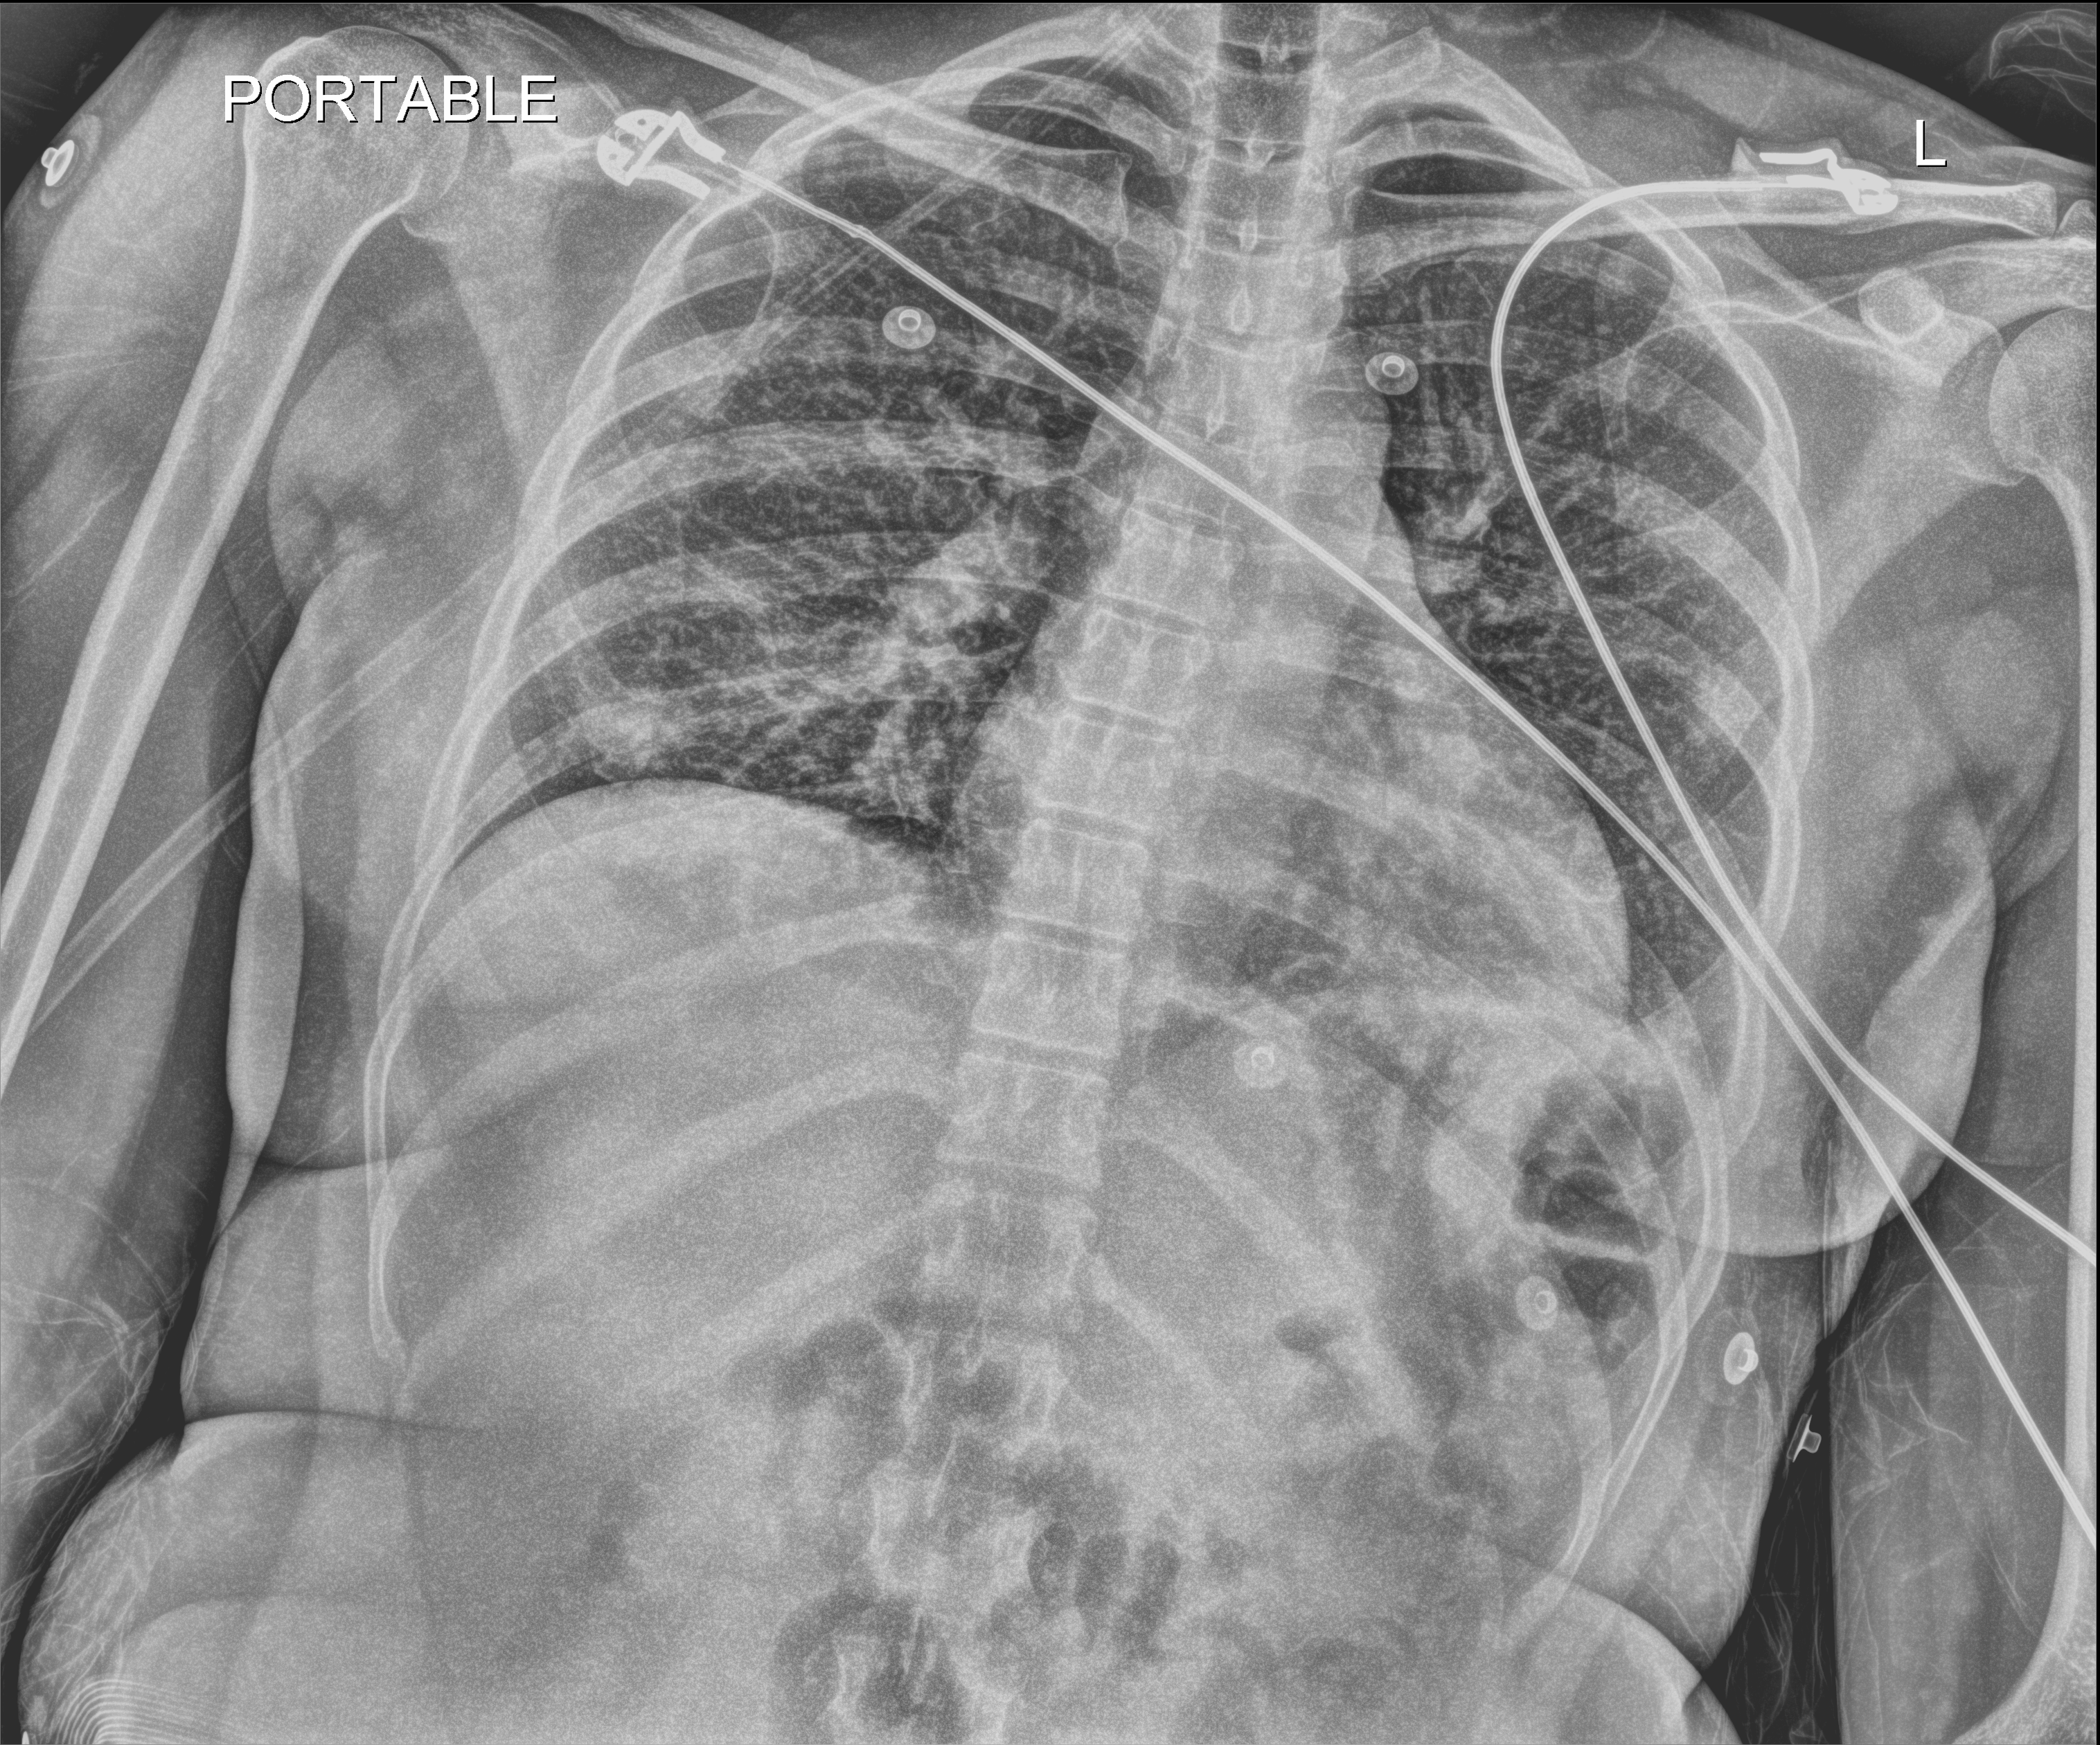
Chest radiograph; anteroposterior (AP) projection. Female patient hospitalised with COVID-19, age 18–59 years.
Admission-level facts for this patient (not findings on this image; timing relative to this image not recorded):
- admitted to intensive care during this hospital stay: no
- mechanically ventilated during this hospital stay: no